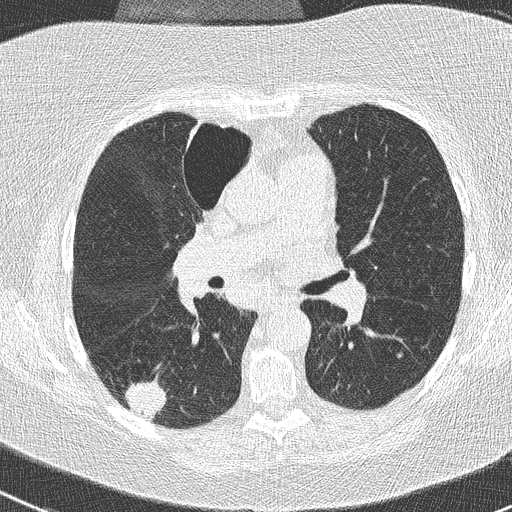
Chest CT (low-dose screening protocol), one axial image; baseline annual screen; lung window (W 1500 / L -600 HU); 2 mm slice thickness; slice 114 of 261 in the series. Female participant, aged 74 years at enrolment. Former smoker at enrolment.
Expert-annotated lung lesion, bounding box [x1, y1, x2, y2] px = [118, 376, 174, 428]. The screening reader recorded 3 non-calcified nodules or masses ≥4 mm on this exam (right lower lobe, right upper lobe, left lower lobe); which of them this box marks is not recorded. Lung cancer was diagnosed 16 days after this screen: non-small cell carcinoma, right lower lobe, poorly differentiated (G3), stage IIIA (AJCC 6th edition), 28 mm at pathology.